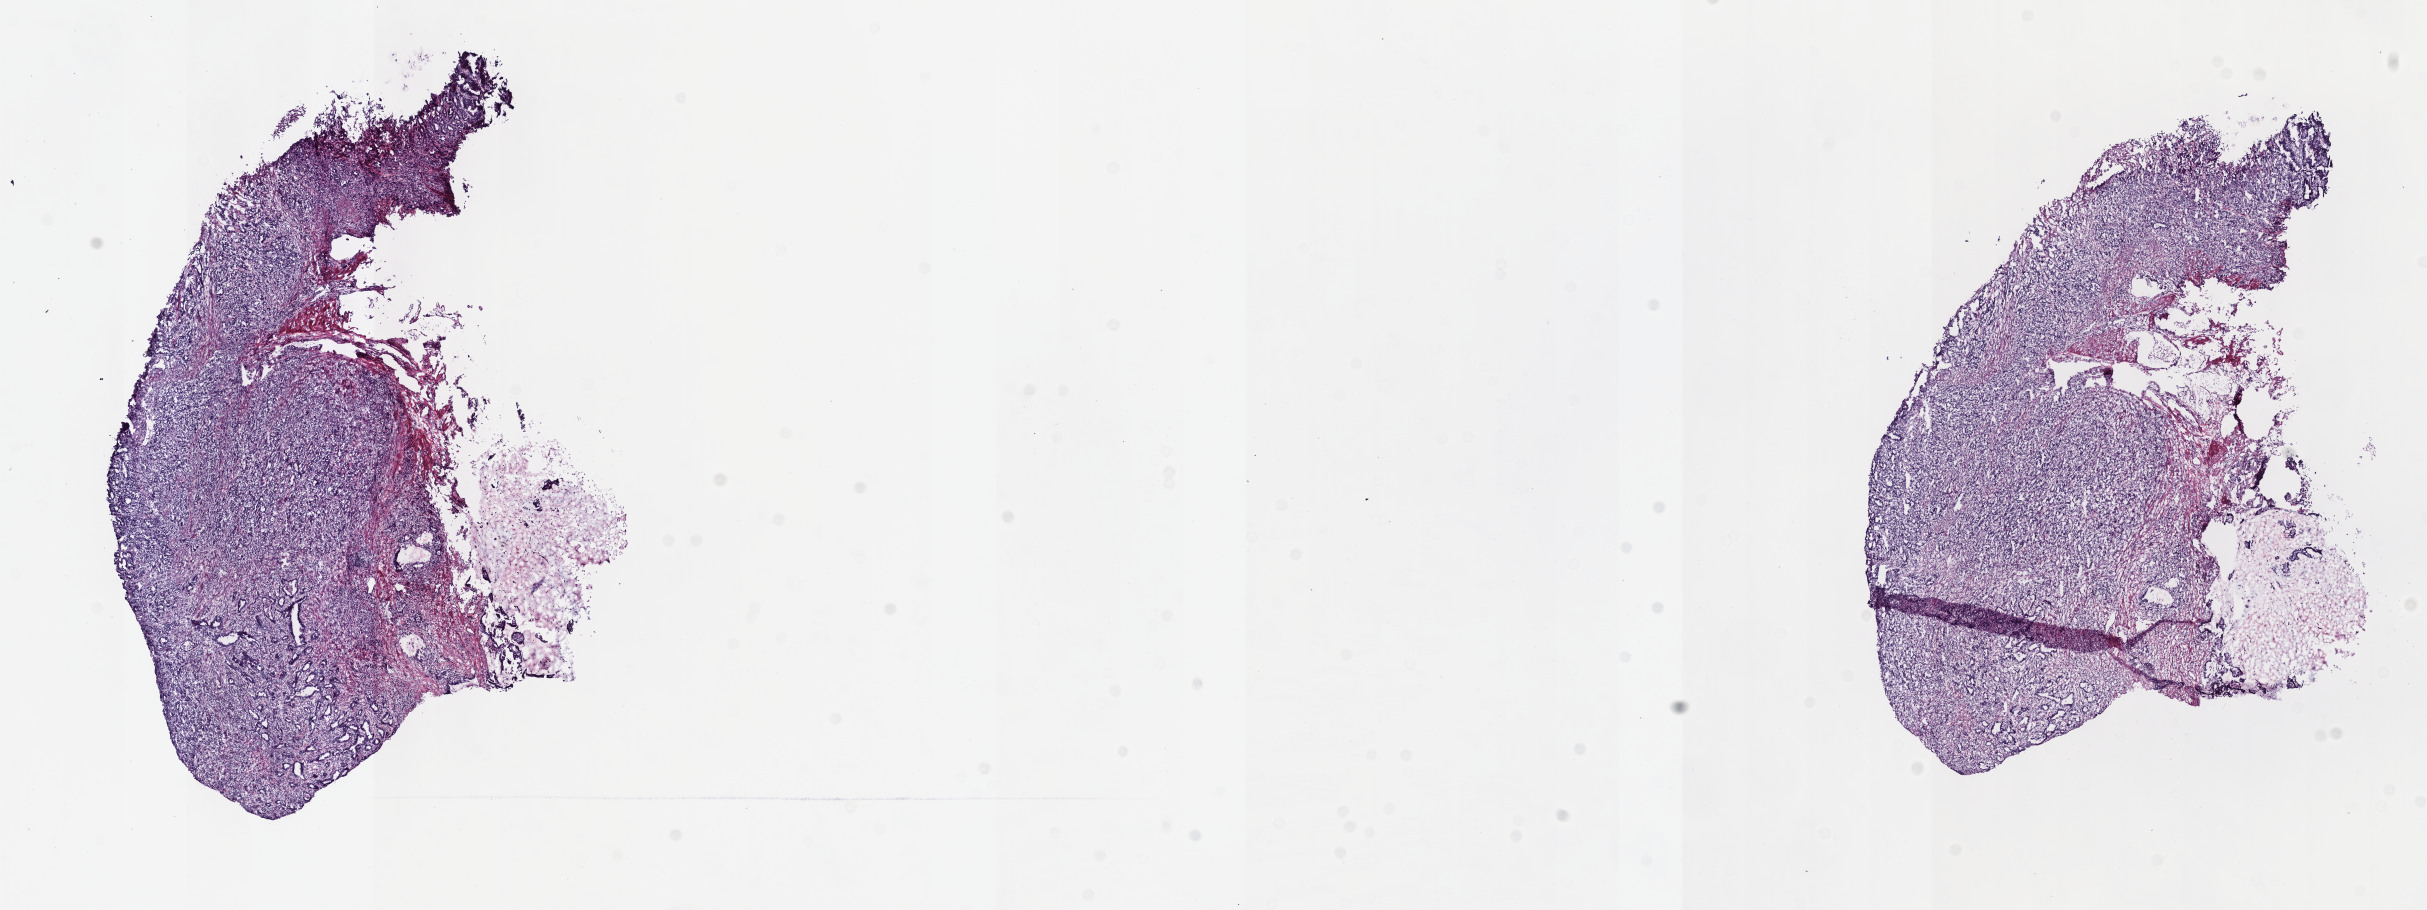
H&E-stained whole-slide image — whole scanned area (about 19.6 x 7.4 mm, from a 40x scan) shown as a low-resolution overview, frozen section from the top of the tissue portion, primary tumour sample from the stomach. Male patient; age at initial diagnosis 69 years. Histologic grade: G2 (moderately differentiated). Composition of this section per pathologist review: tumour cells 70%, tumour nuclei 80%, normal cells 10%, stromal cells 20%, necrosis 0%. Infiltration values recorded for this section: lymphocyte infiltration 0%, monocyte infiltration 0%, neutrophil infiltration 0%.
AJCC pathologic stage: II (6th edition). Diagnosis: Tubular adenocarcinoma (gastric antrum). Lymph nodes positive (case pathology): 0 of 27 examined.